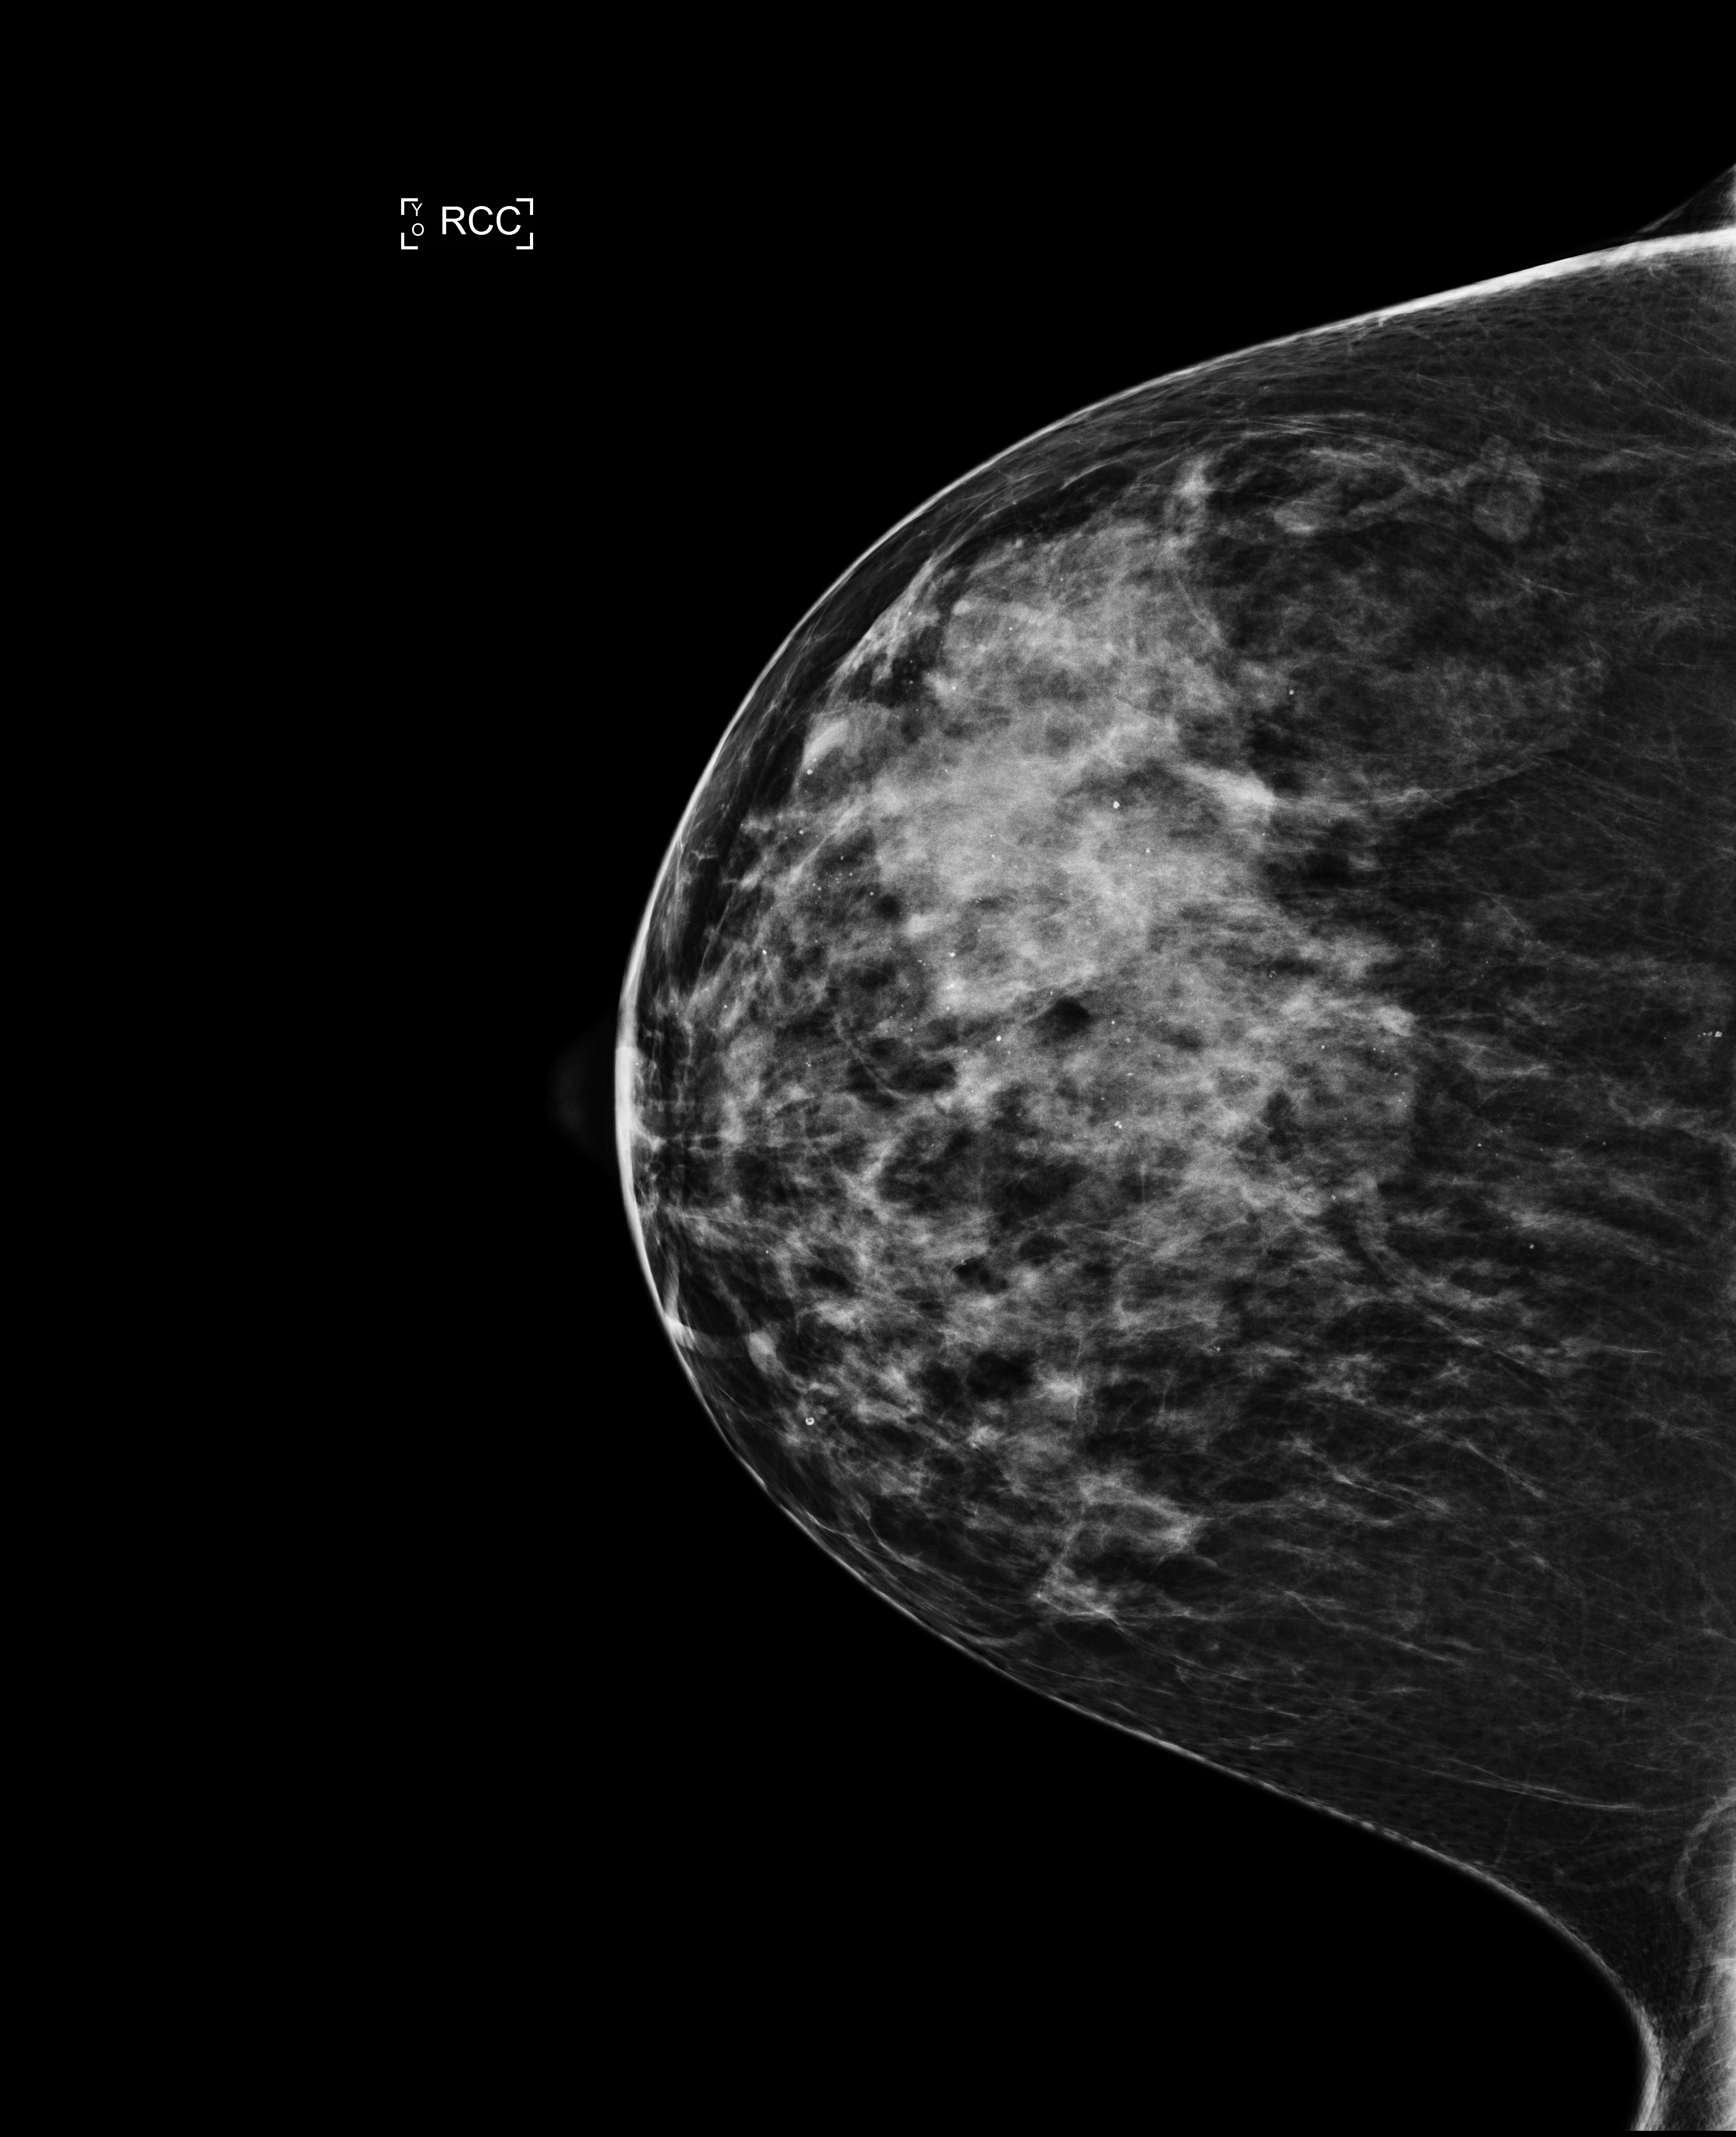
Digital mammogram (FFDM), right breast, craniocaudal (CC) view, annual screening mammography examination, system: Selenia Dimensions. Female patient, age 45 years.
Breast density at the screening exam (both breasts): heterogeneously dense (BI-RADS density category c). Final BI-RADS assessment for this screening round (tomosynthesis exam, both breasts): category 2. Recall: no recall after this screen.